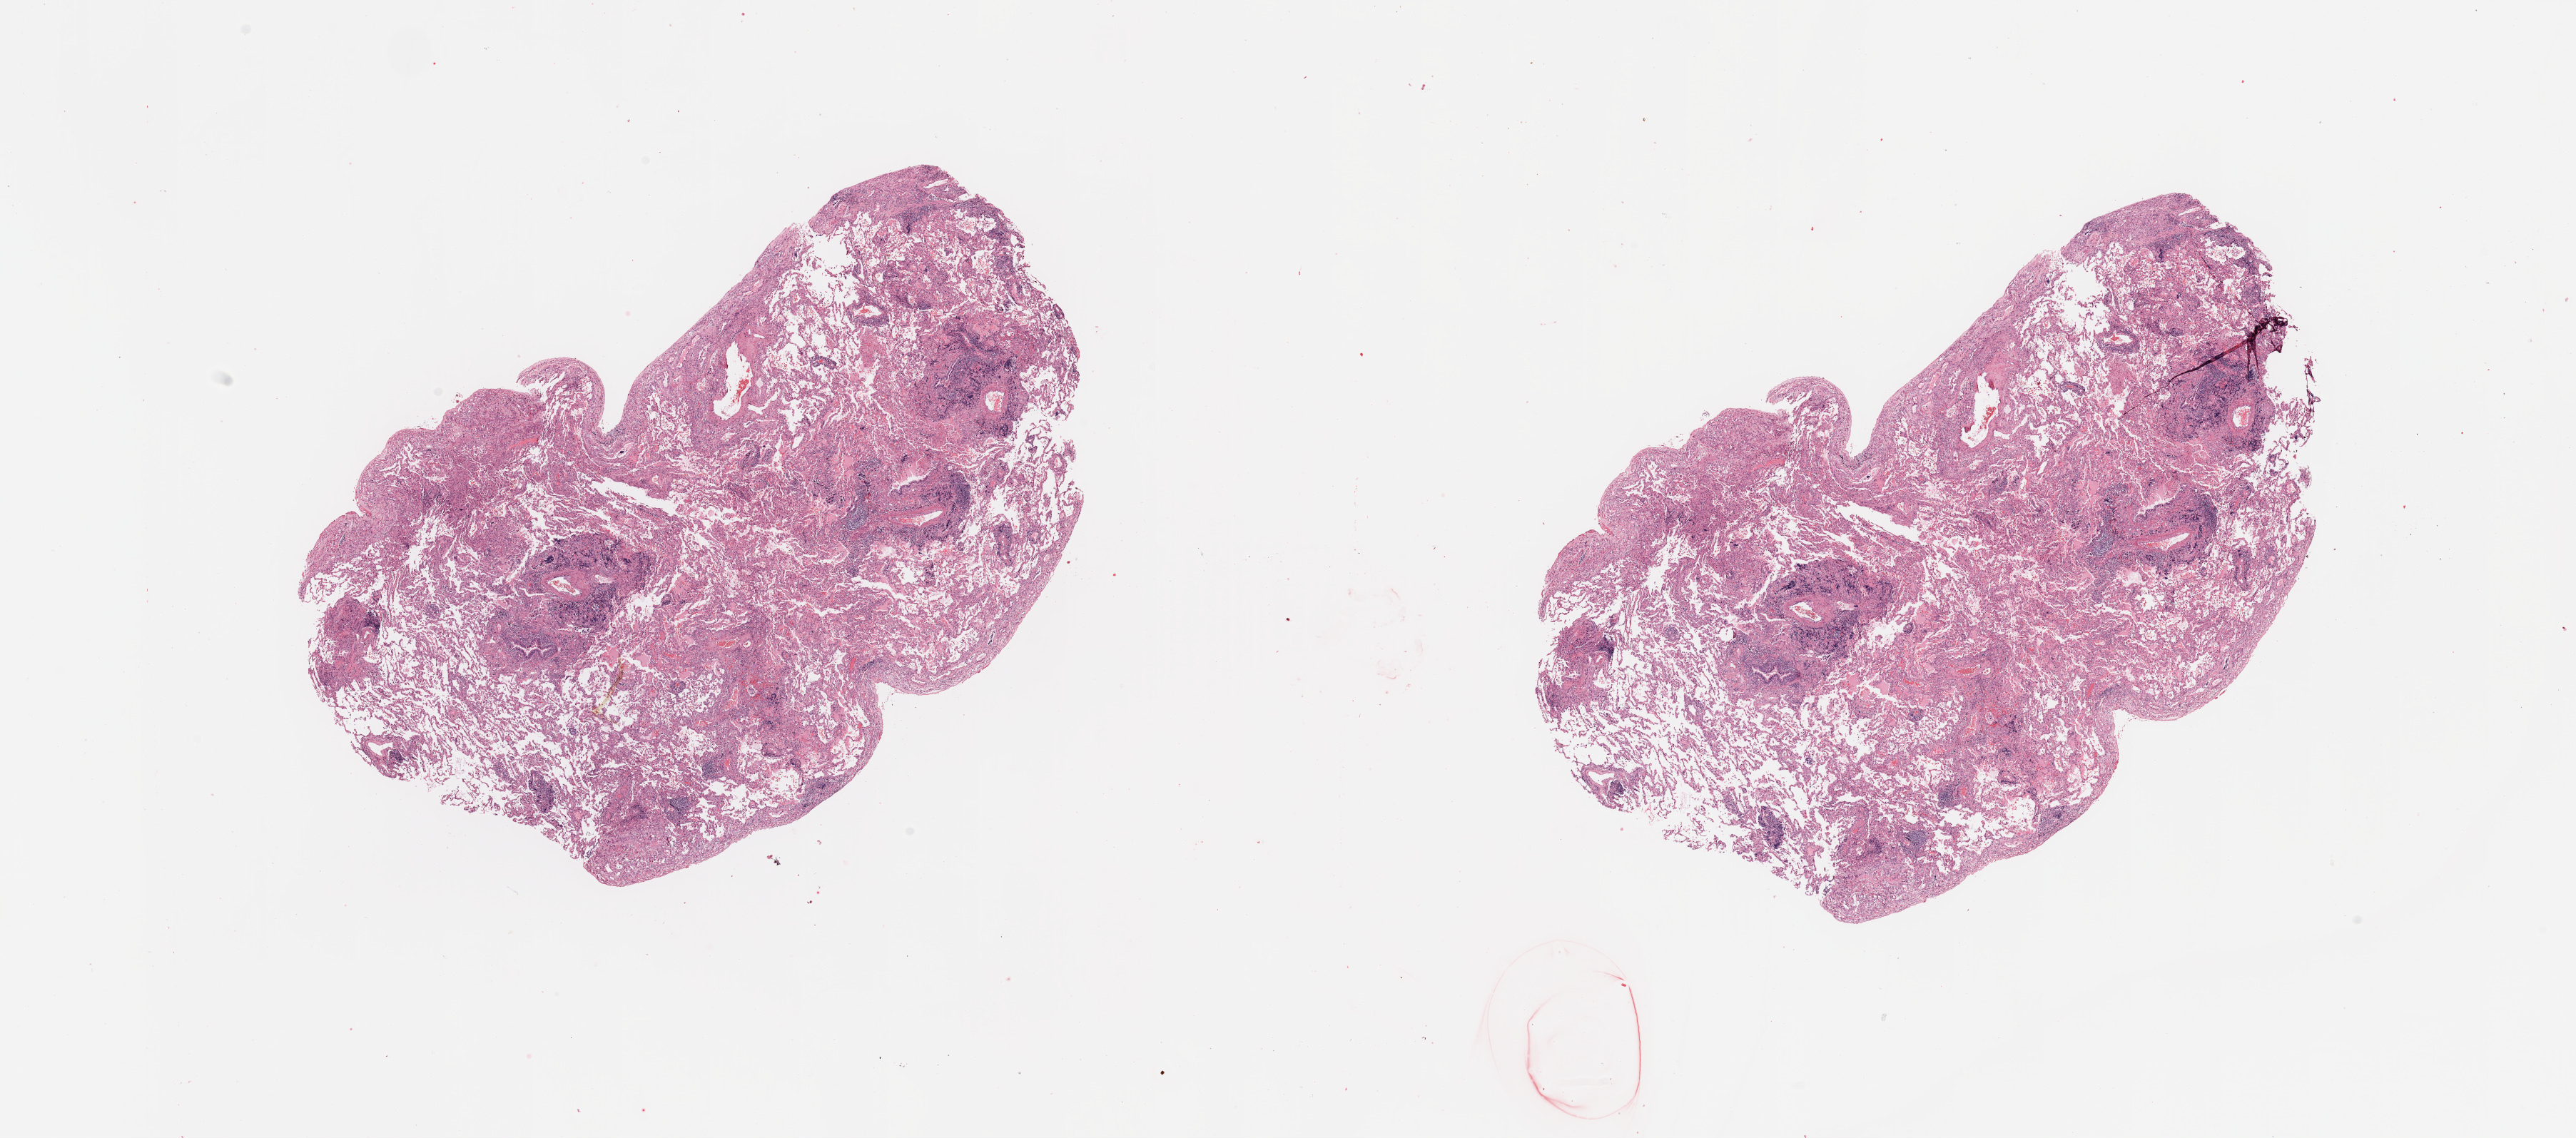
Whole-slide histology image, Hematoxylin and eosin (H&E) stained, a low-resolution overview of the entire scanned area, about 28.5 x 12.6 mm. Normal (non-tumour) tissue sample, sampled site: lung. 63-year-old male patient.
• this section: normal (non-tumour) tissue from the same patient
• patient diagnosis: Adenocarcinoma, NOS